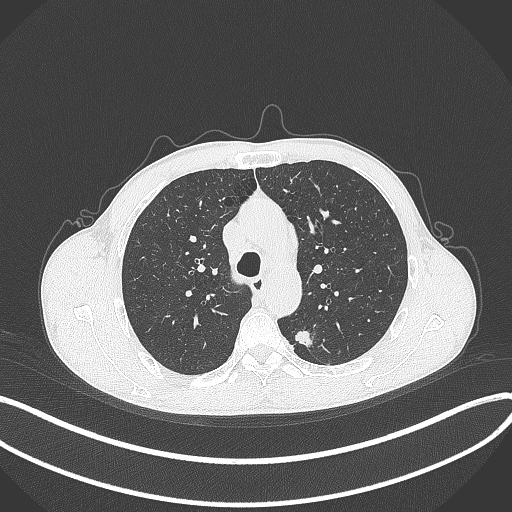
Chest CT, one axial slice; slice 281 of 429 in the series (ordered by position); reconstruction kernel B70f; lung window (W 1500 / L -600 HU); 512 × 512 image matrix, field of view 400 × 400 mm. Patient: male, 51 years. Case-level facts recorded for this patient, not image findings: clinical TNM (as recorded): T2a N1 M1.
Structures marked on this image (bounding box drawn by a radiologist):
- lung tumour (recorded histology: adenocarcinoma): bounding box <291,327,315,351> (left, top, right, bottom; pixels)